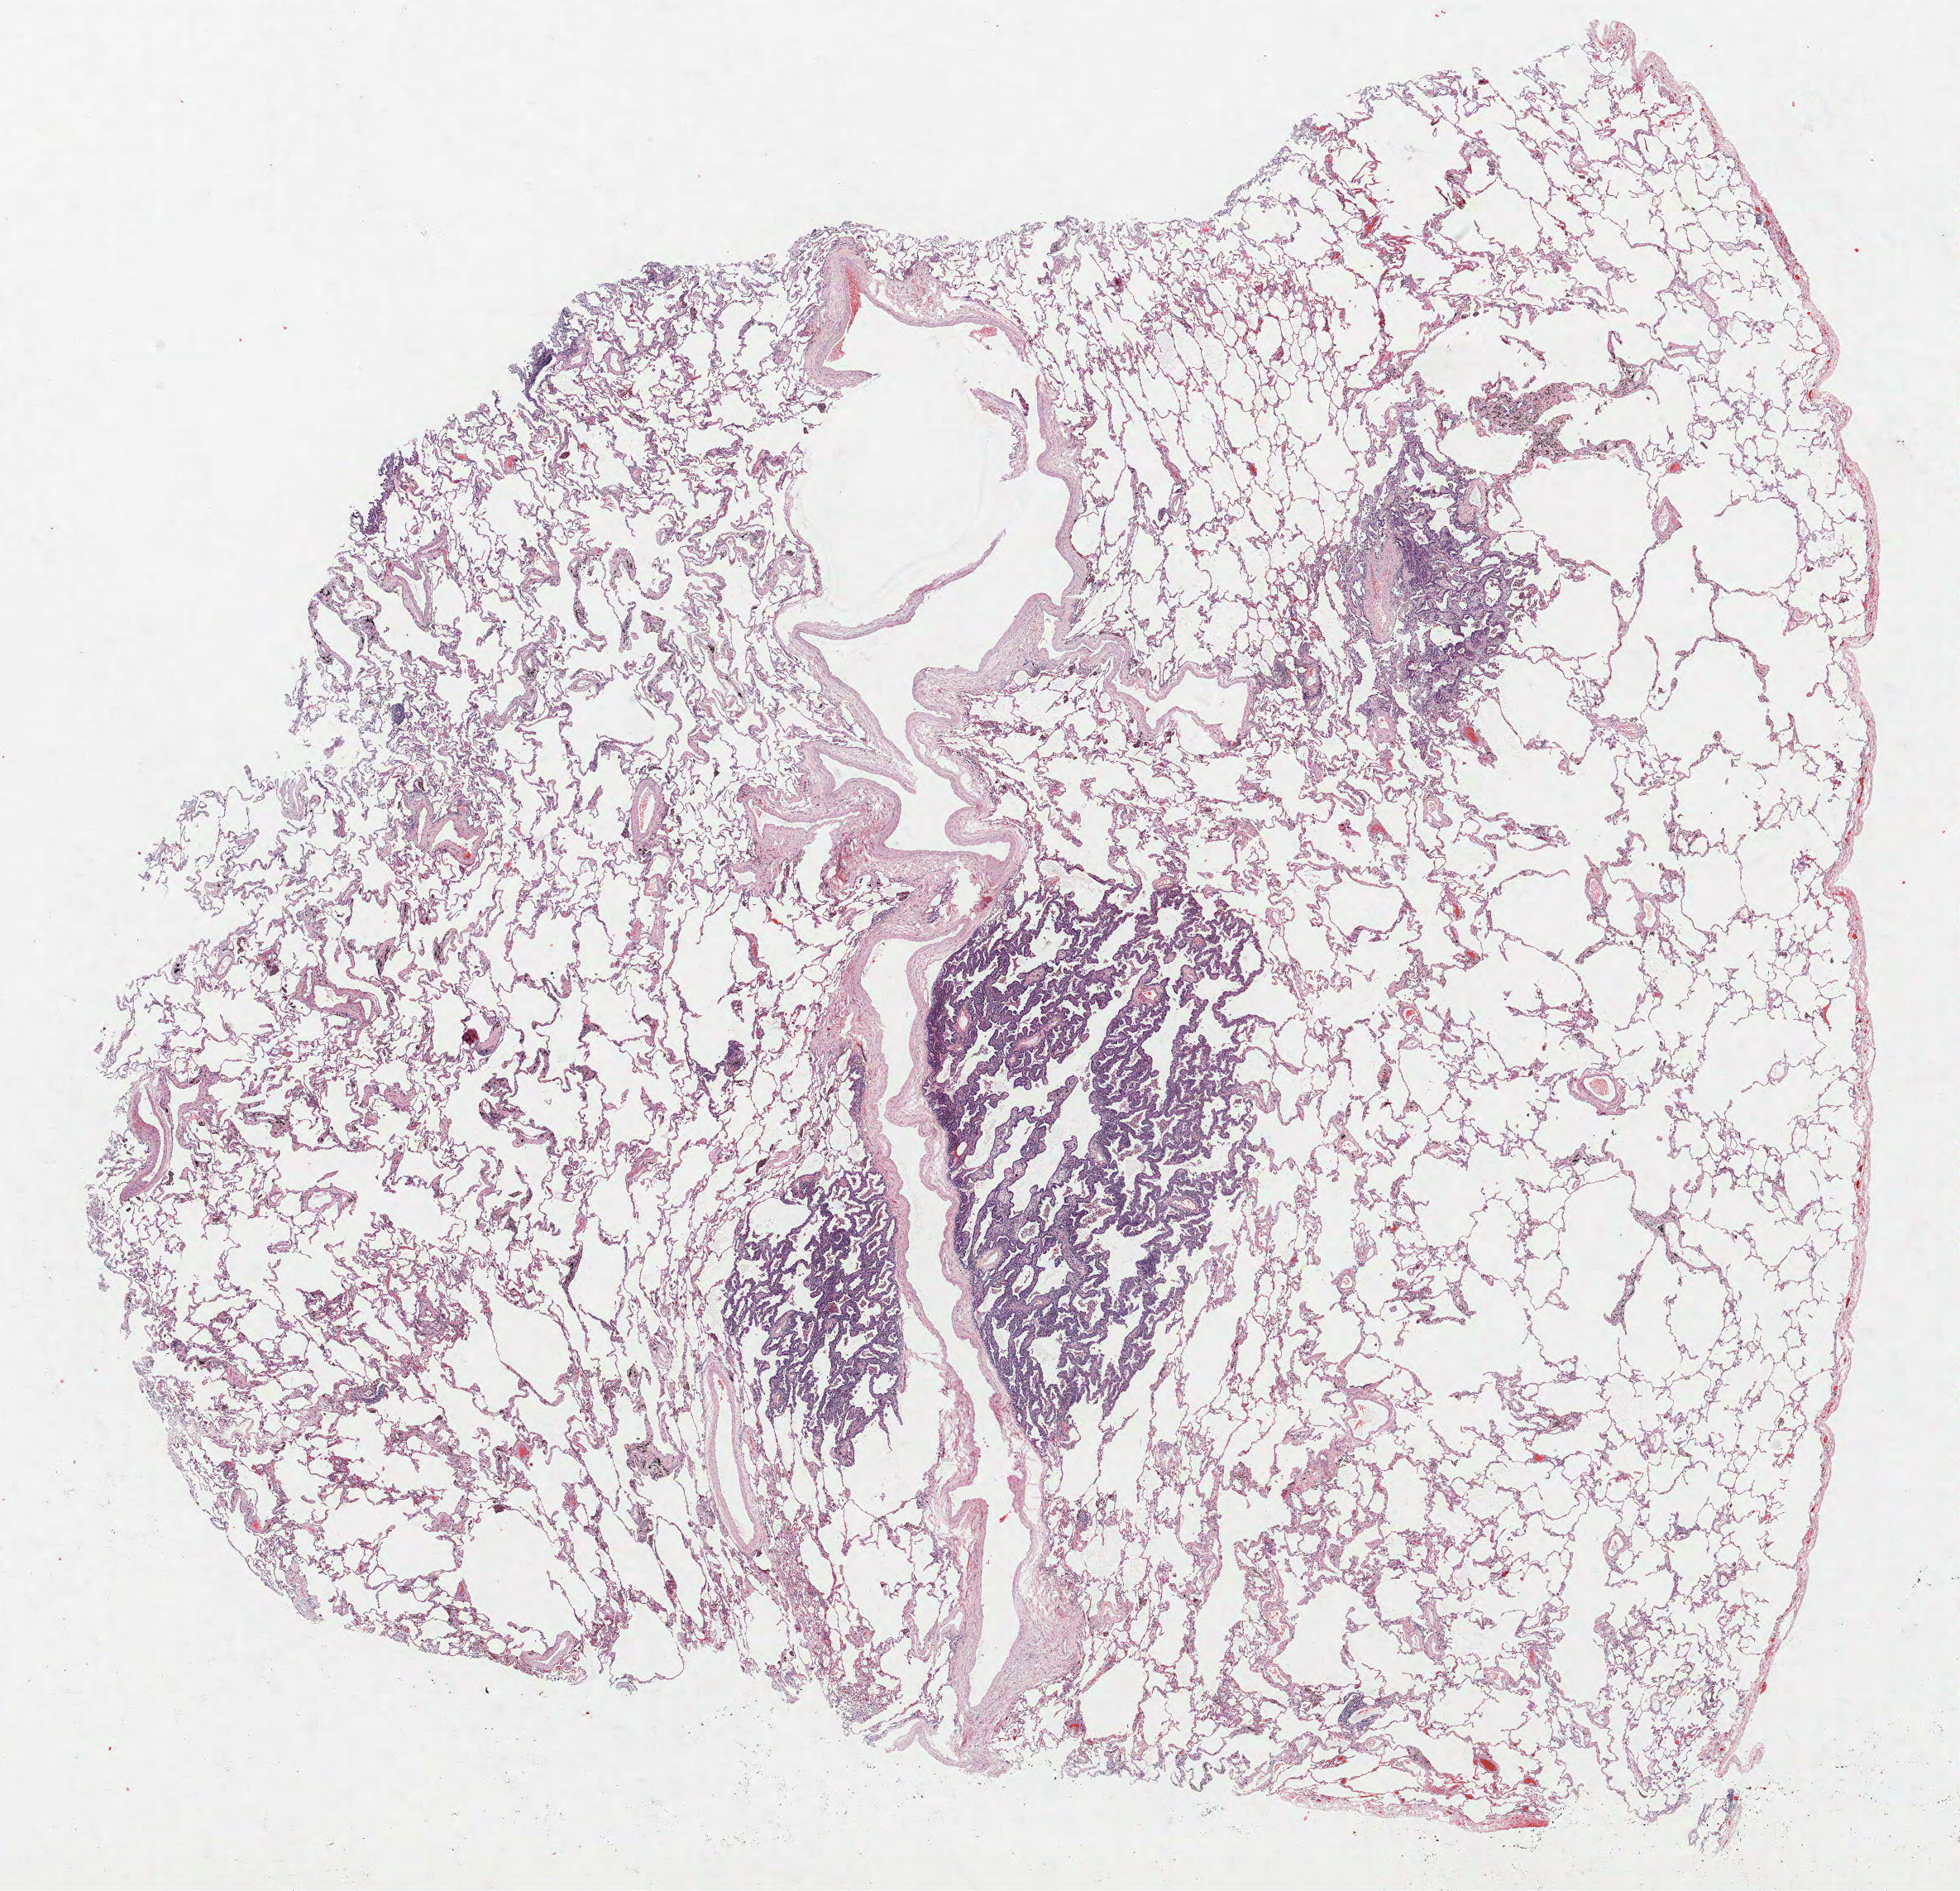
Whole-slide histology image, Hematoxylin and eosin (H&E) stained, whole scanned area (about 19.0 x 18.3 mm) shown as a low-resolution overview. FFPE section. Lung tissue. Female, age 67 at enrolment. Grade: well differentiated (G1).
Tumour size (pathology): 25 mm. Participant's lung-cancer diagnosis: Bronchiolo-alveolar adenocarcinoma, NOS (ICD-O-3 8250/3). Primary tumour location (clinical record): right middle lobe. Stage (AJCC 6th edition): IA. ICD-O-3 topography: middle lobe of lung (C34.2).